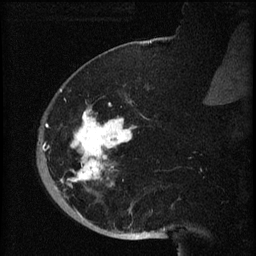
Breast MRI (dynamic contrast-enhanced), one sagittal slice; position 19 of 60 along the scan axis; dynamic contrast-enhanced series, image 2 of 3 at this slice position (ordered by acquisition); 1.5 T; TE 4.2 ms, TR 8.2 ms; 2 mm slice thickness; 256 × 256 image matrix, field of view 180 × 180 mm. Female patient, age 71 years.
Structures marked on this image (semi-automatically segmented with operator editing):
- analysis volume of interest (the breast-tissue region the enhancement analysis was run in; not a lesion): box from (x=40, y=72) to (x=148, y=196) px
- tumour enhancement mask (voxels above the 70 % enhancement threshold inside the analysis volume of interest): (x=42, y=89)–(x=136, y=186)